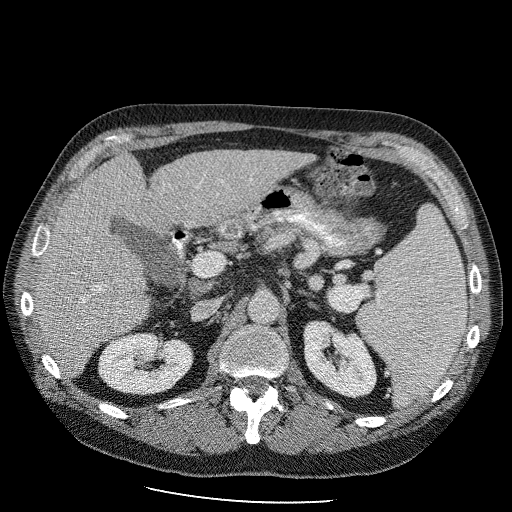
Contrast-enhanced abdominal CT (liver protocol), one axial slice. Position 49 of 98 along the scan axis. Reconstruction kernel STANDARD. Soft-tissue window (W 400 / L 40 HU). 512 × 512 image matrix, field of view 400 × 400 mm. Case-level facts recorded for this patient, not image findings: diagnosis: hepatocellular carcinoma (patient treated with transarterial chemoembolisation; whether this scan precedes or follows treatment is not stated here); TNM stage (as recorded): Stage-II; Child-Pugh class: B.
Outlined on this slice (semi-automatically segmented with operator editing):
- liver parenchyma outside the tumour (the mass and vessels are separate outlines, so this box may not span the whole liver): bounding box (x1, y1, x2, y2) in pixels: (32, 148, 318, 376)
- liver vessels: (40, 186, 197, 295)